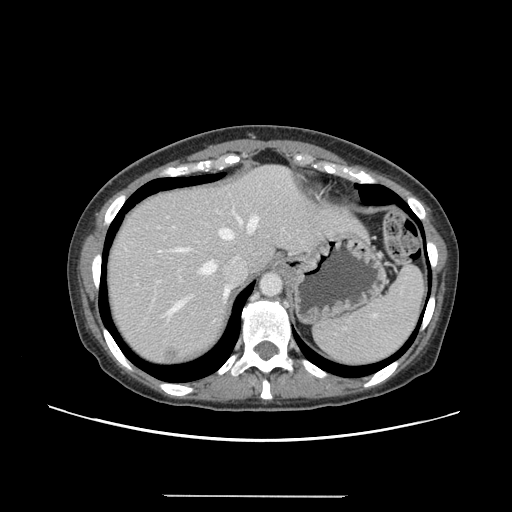
Contrast-enhanced abdominal CT, one axial slice; position 117 of 144 along the scan axis; intravenous contrast given; soft-tissue window (W 400 / L 40 HU); 2.5 mm slice thickness; 512 × 512 image matrix. Female patient, age 53 years. Case-level facts recorded for this patient, not image findings: diagnosis: colorectal cancer liver metastases, imaged before liver resection; multiple liver metastases: yes; largest metastasis: 1.1 cm; disease in both lobes: no.
Structures marked on this image (manually delineated by an expert):
- hepatic veins: bounding box (x1, y1, x2, y2) in pixels: (159, 215, 259, 313)
- liver: (107, 166, 365, 365)
- planned liver remnant (the part of the liver to remain after resection): (107, 166, 288, 299)
- portal vein (with intrahepatic branches): (157, 227, 175, 283)
- liver metastasis: (164, 348, 178, 362)